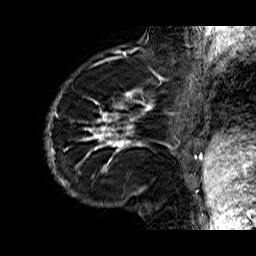
Breast MRI (dynamic contrast-enhanced), one sagittal slice. Position 10 of 60 along the scan axis. Dynamic contrast-enhanced series, time point 2 of 6 at this slice position (early post-contrast). 1.5 T. TE 6.3 ms, TR 32.9 ms. 256 × 256 image matrix, field of view 200 × 200 mm. Female patient. From the clinical record (not read from this slice): setting: breast cancer imaged before/during neoadjuvant chemotherapy; receptor status: HR-positive, HER2-negative.
Outlined on this slice (semi-automatically segmented with operator editing):
- analysis volume of interest (the breast-tissue region the enhancement analysis was run in; not a lesion): box from (x=46, y=74) to (x=176, y=210) px
- tumour enhancement mask (voxels above the 100 % enhancement threshold inside the analysis volume of interest): (x=46, y=88)–(x=176, y=194)